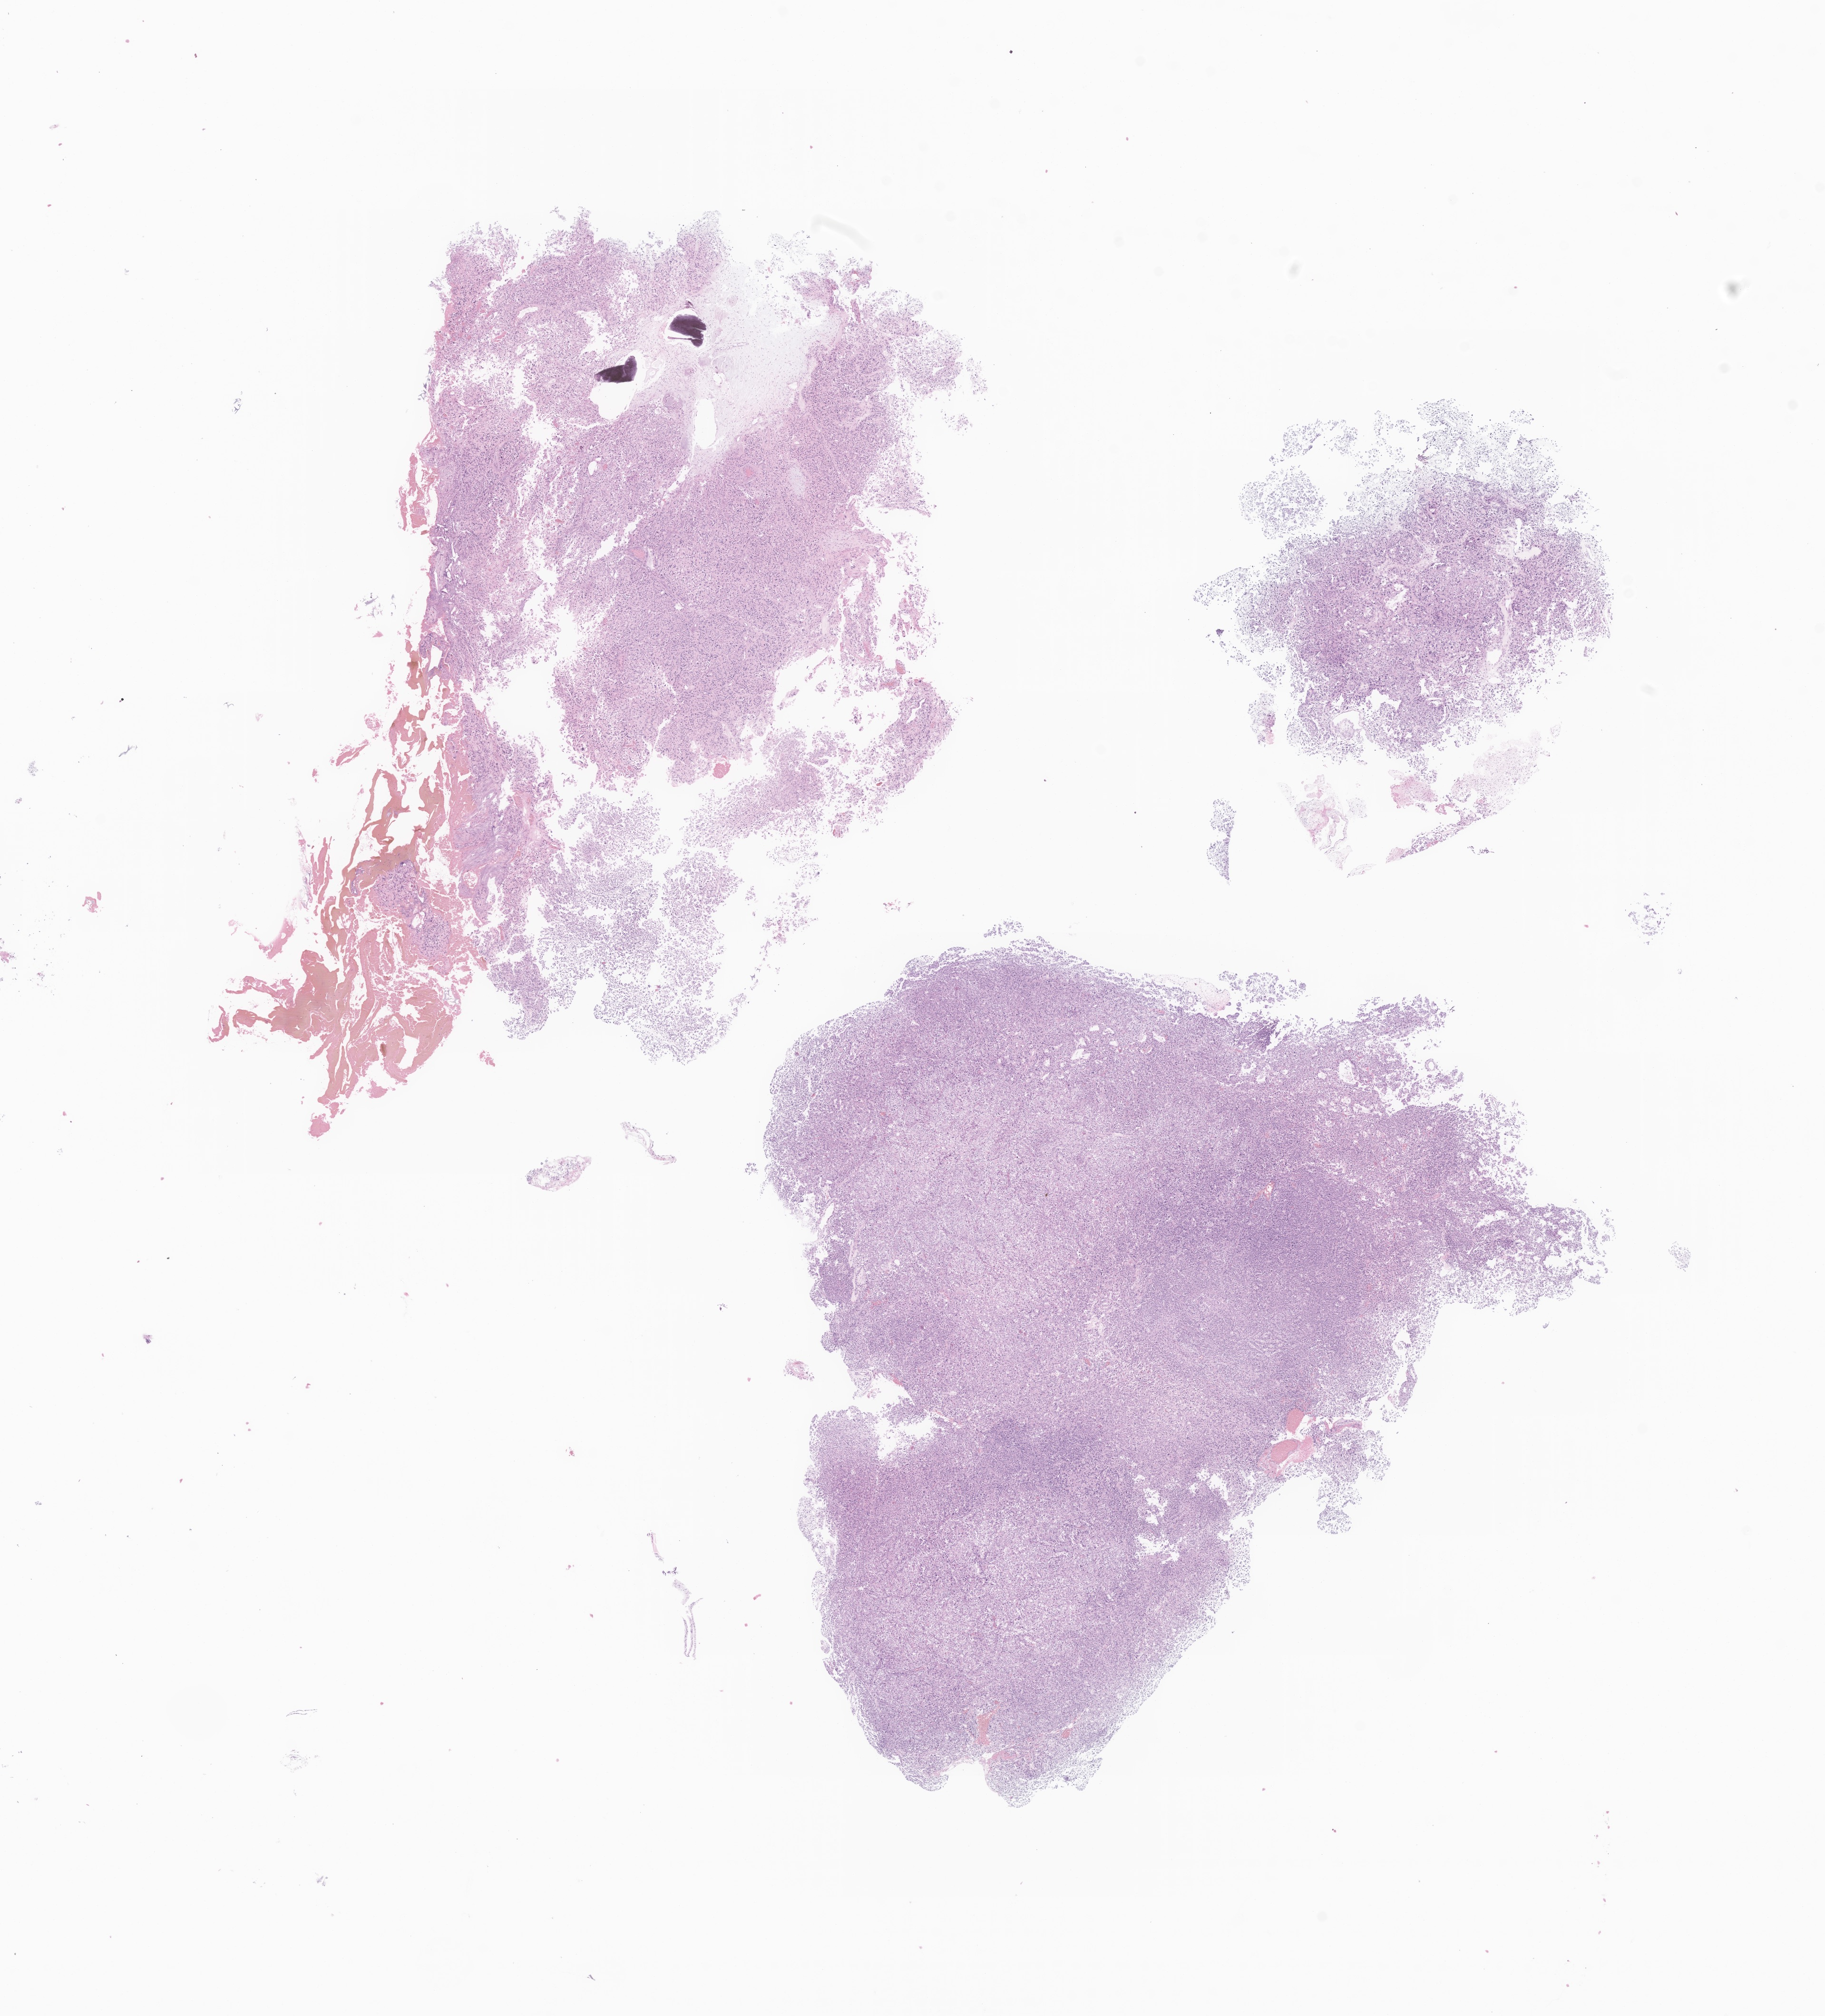
Whole-slide image, hematoxylin and eosin (H&E) stain of tumor tissue from the brain, shown as a low-resolution overview of the whole scanned area (about 16.2 x 17.9 mm); FFPE section. Patient: male, age 82 months (6 years 10 months).
Diagnosis: Choroid plexus carcinoma.